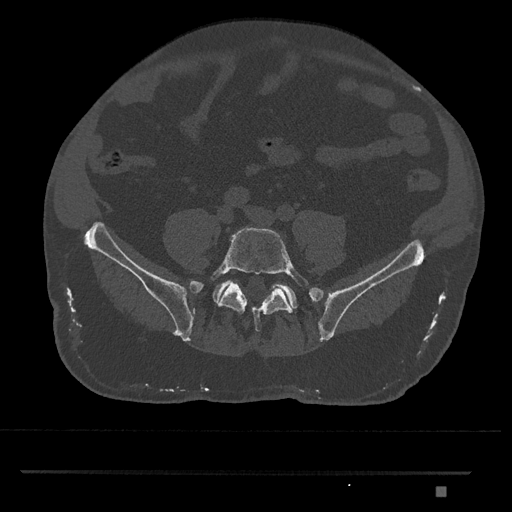
CT including the spine, one axial slice; position 548 of 1134 along the scan axis; reconstruction kernel Br40s/3; 120 kVp; bone window (W 1800 / L 400 HU); 0.5 mm slice thickness; 512 × 512 image matrix. Patient: male, 65 years. From the clinical record (not read from this slice): primary cancer: prostate.
Structures marked on this image (semi-automatically segmented with operator editing):
- L5 vertebra: bounding box [x1, y1, x2, y2] px = [210, 227, 311, 332]